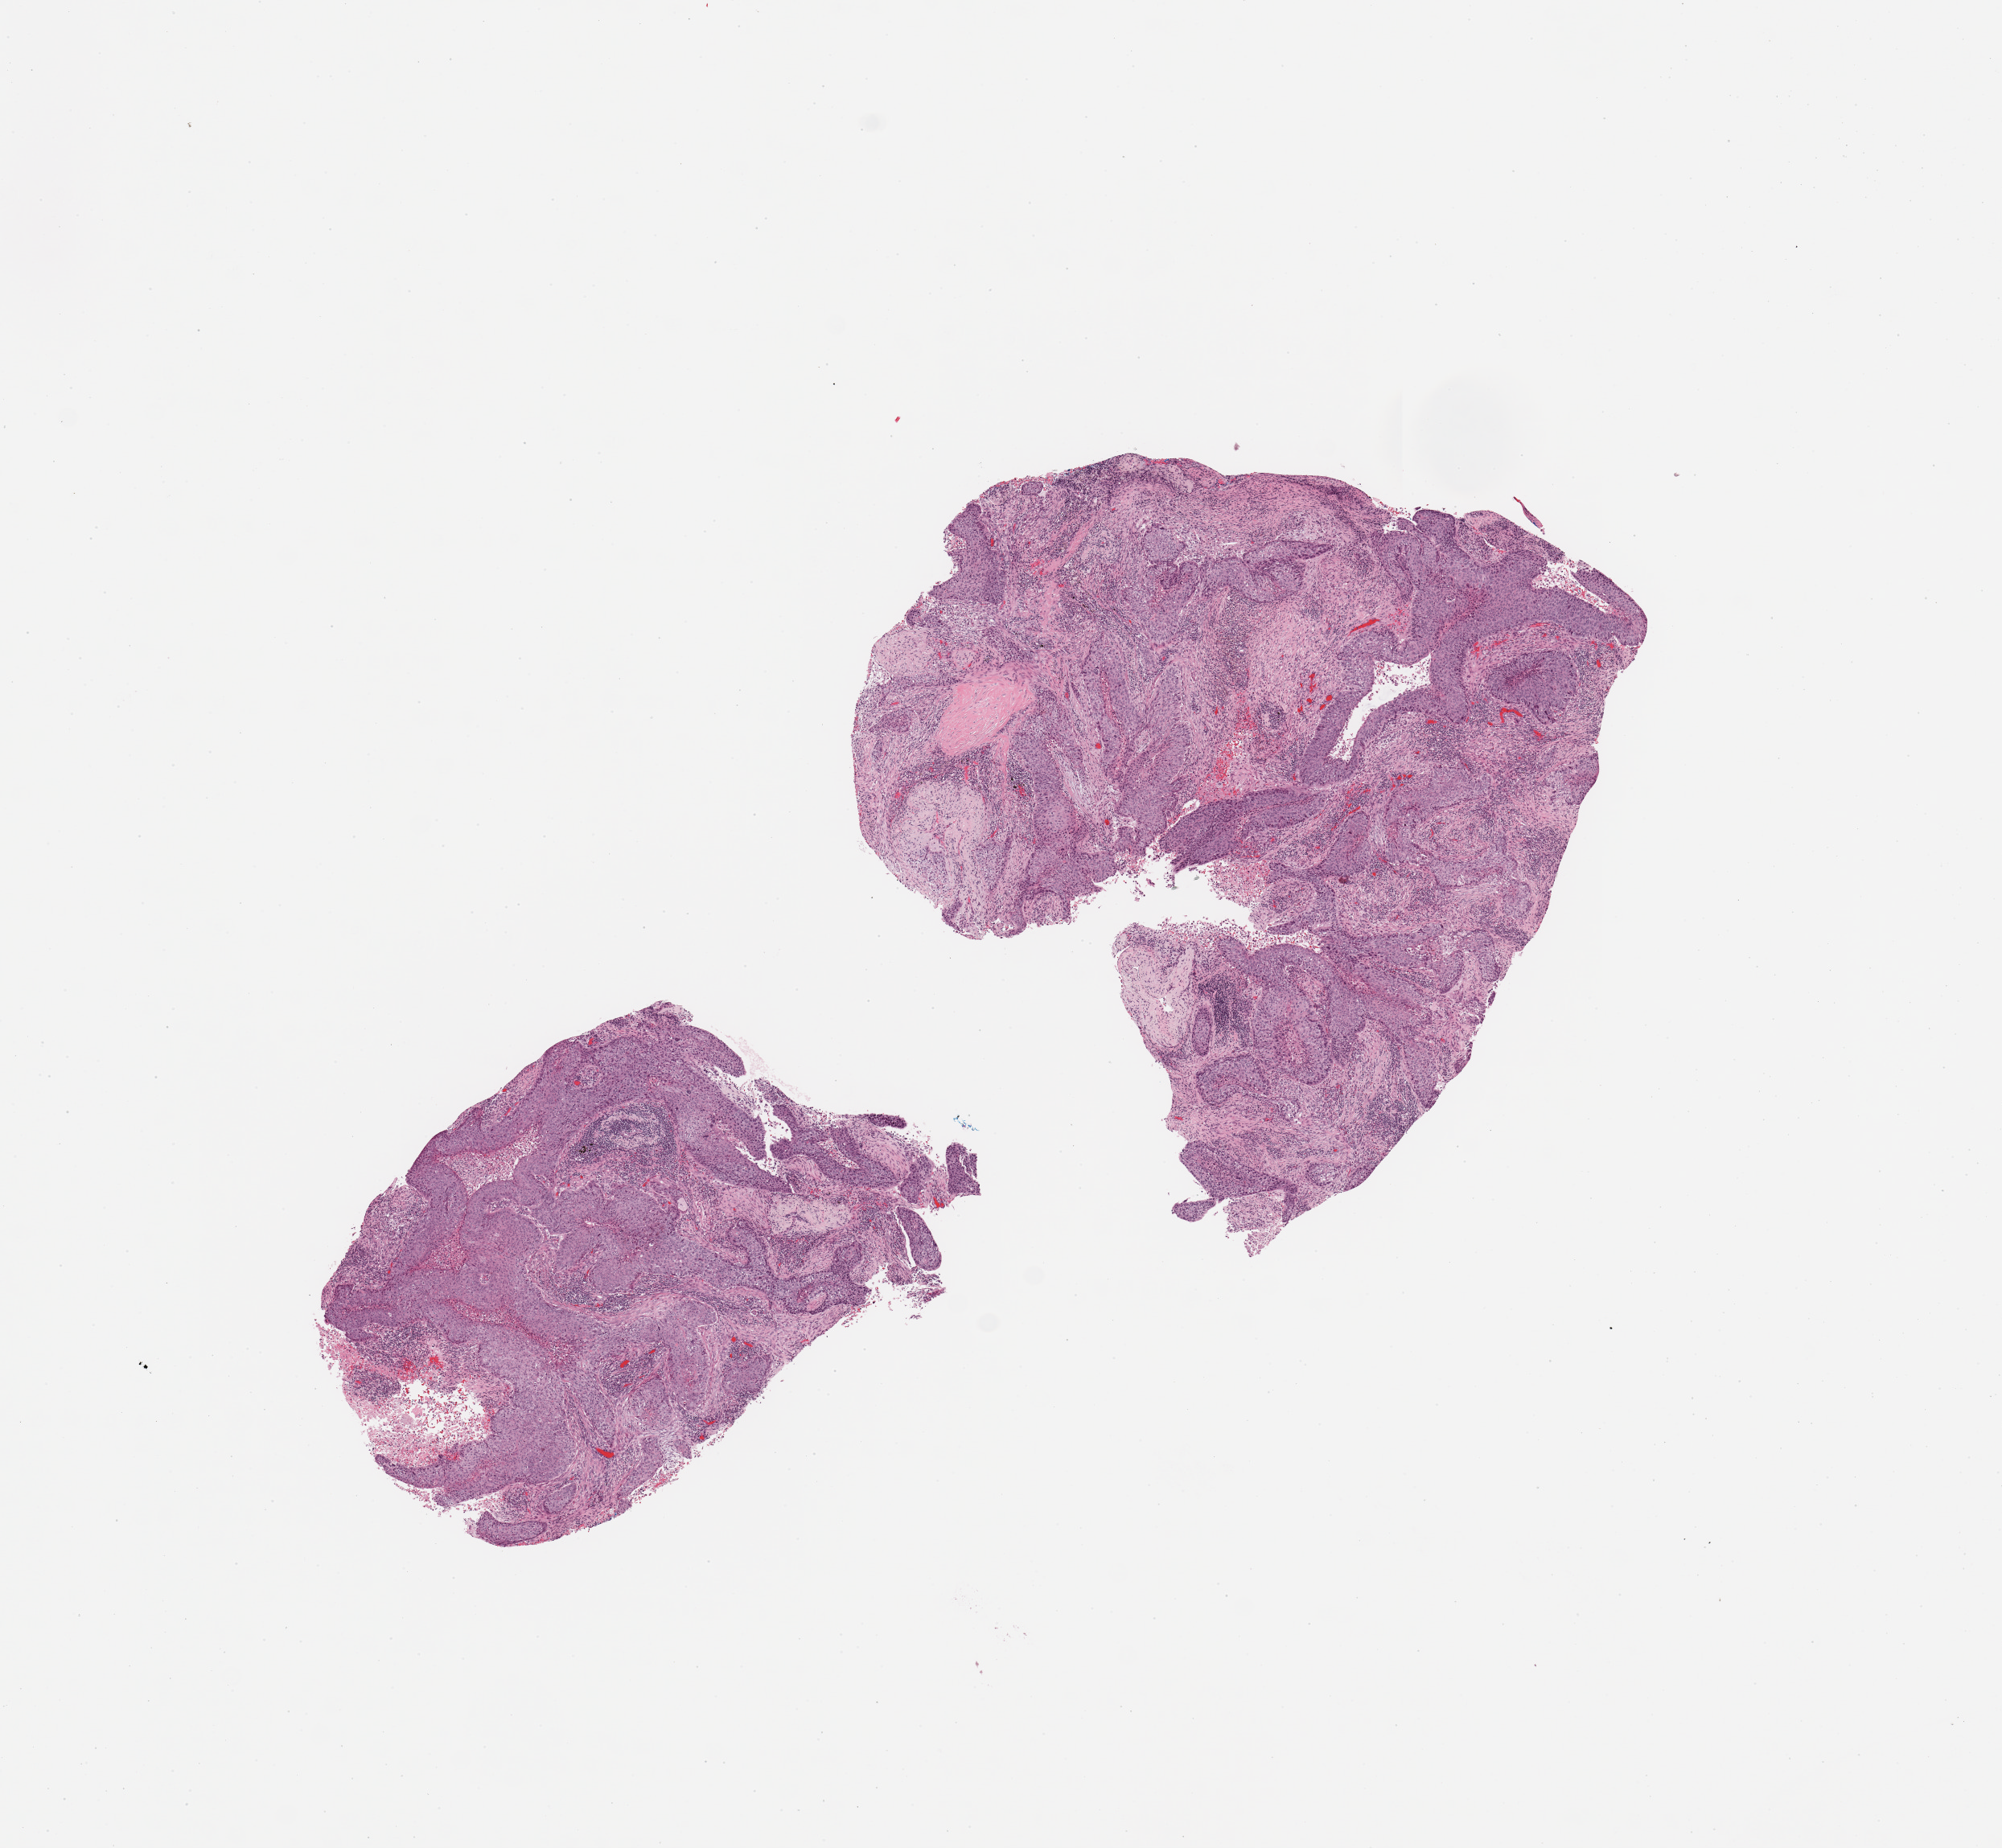
H&E whole-slide image, low-resolution overview of the scanned area, about 9.8 x 9.1 mm (acquisition: 20x scan). Tumour tissue sample, lung. Female, 74 y/o. Histologic grade: G2 (moderately differentiated).
* primary tumour site (as recorded): right upper lobe
* AJCC pathologic stage: IB
* diagnosis: Squamous cell carcinoma, NOS